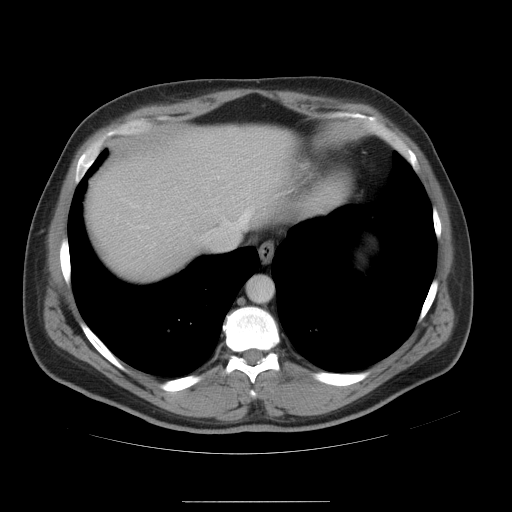
Contrast-enhanced abdominal CT, one axial slice. Slice 45 of 54 in the series (ordered by position). Intravenous contrast given. Soft-tissue window (W 400 / L 40 HU). 5 mm slice thickness. 512 × 512 image matrix, field of view 436 × 436 mm. Male patient, age 40 years. From the clinical record (not read from this slice): diagnosis: colorectal cancer liver metastases, imaged before liver resection; multiple liver metastases: no; largest metastasis: 15 cm; disease in both lobes: no.
Structures marked on this image (expert manual segmentation):
- hepatic veins: box from (x=137, y=209) to (x=251, y=240) px
- liver: (x=86, y=126)–(x=300, y=284)
- planned liver remnant (the part of the liver to remain after resection): (x=167, y=126)–(x=300, y=254)